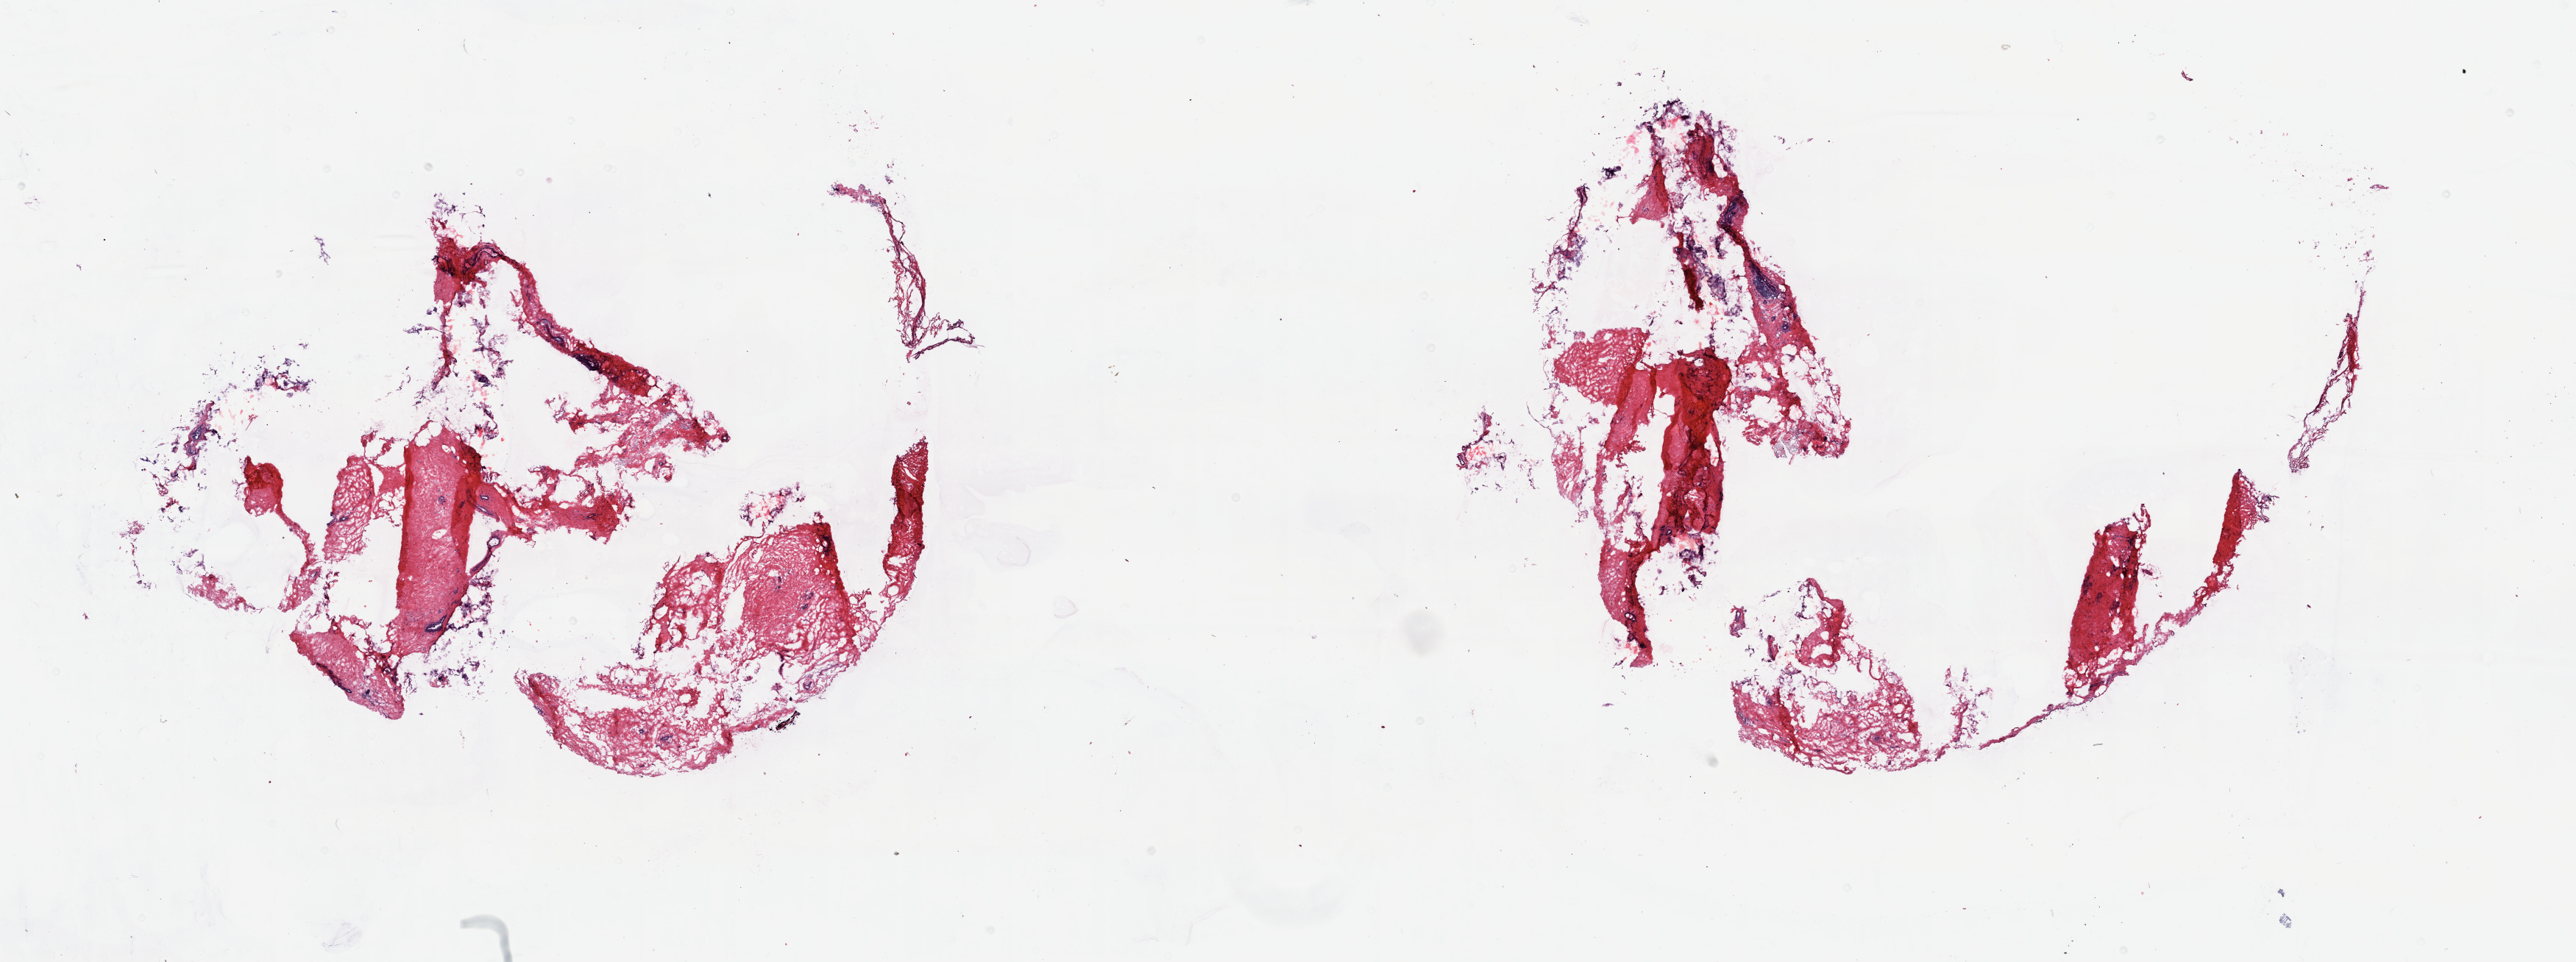
H&E whole-slide image — shown as a low-resolution overview of the whole scanned area (about 27.8 x 10.4 mm, slide scanned at 20x); frozen section; sample: solid tissue normal (non-tumour tissue), breast. Female, age 79 years at initial diagnosis. Slide review estimates, as recorded: tumour cells 0%, normal cells 100%. Inflammatory infiltration, as recorded: lymphocyte infiltration 35%, monocyte infiltration 2%, neutrophil infiltration 0%.
- this section: solid tissue normal (non-tumour) sample from the same patient
- patient diagnosis: Infiltrating duct carcinoma, NOS